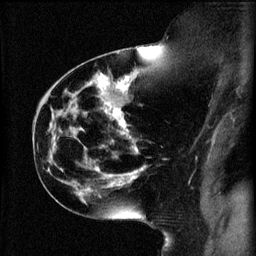
Breast MRI (dynamic contrast-enhanced), one sagittal slice; position 33 of 60 along the scan axis; 3 images stored at this slice position (order not interpretable as contrast timing); 1.5 T; TE 4.2 ms, TR 11 ms; 2 mm slice thickness; 256 × 256 image matrix. Patient: female, 44 years.
Outlined on this slice (semi-automatically segmented with operator editing):
- analysis volume of interest (the breast-tissue region the enhancement analysis was run in; not a lesion): bounding box <110,124,145,179> (left, top, right, bottom; pixels)
- tumour enhancement mask (voxels above the 70 % enhancement threshold inside the analysis volume of interest): <110,124,143,179>